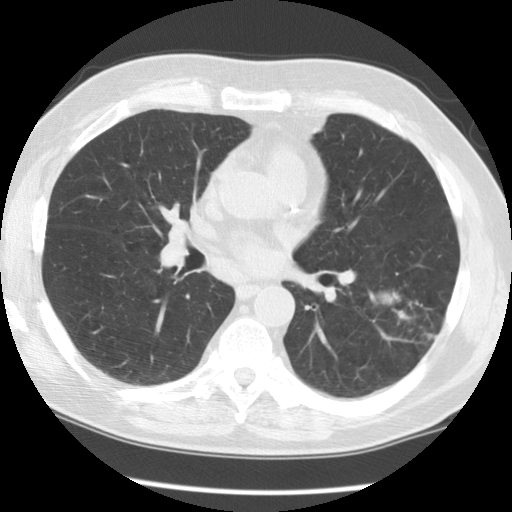
Chest CT (low-dose screening protocol), one axial image. Baseline screening round. Lung window (W 1500 / L -600 HU). Slice 60 of 130 in the series. 512 × 512 image matrix, field of view 340 × 340 mm. Male, age 71 years at enrolment. Former smoker at enrolment.
• Expert-annotated lung lesion, box from (x=368, y=269) to (x=462, y=365) px.
• The screening reader recorded 3 non-calcified nodules or masses ≥4 mm on this exam (left lower lobe, right upper lobe, right upper lobe); which of them this box marks is not recorded.